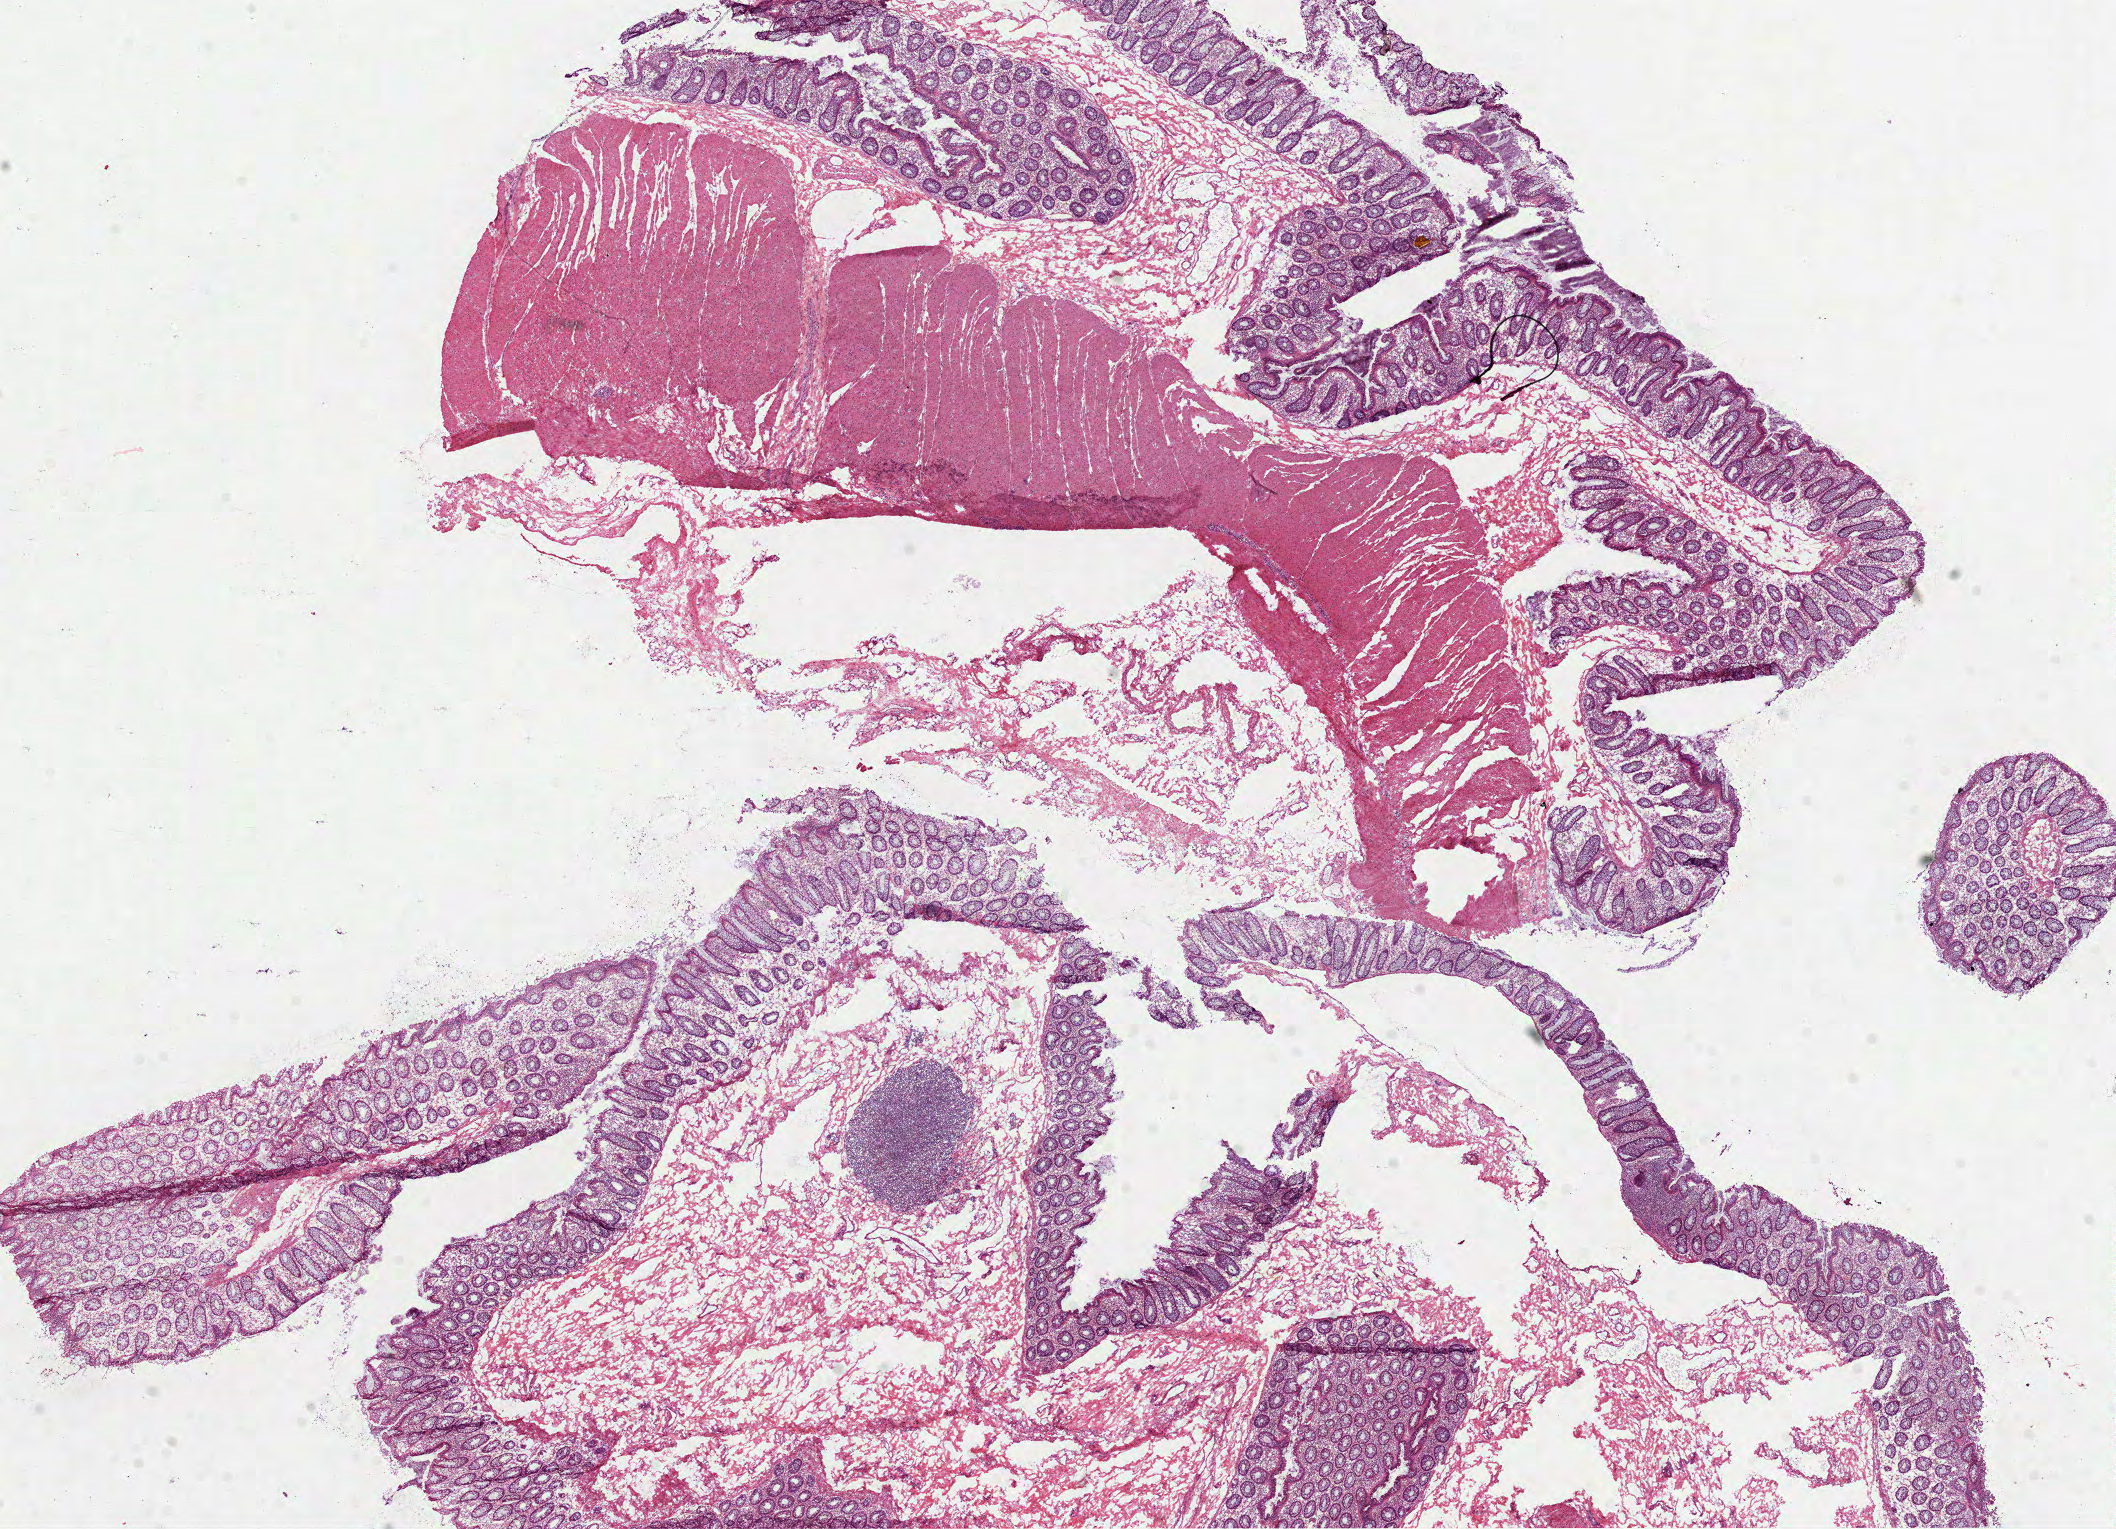
Digitized Hematoxylin and eosin (H&E) stained tissue section (whole slide) — shown as a low-resolution overview of the whole scanned area (about 17.1 x 12.3 mm, from a 40x scan), frozen section from the top of the tissue portion, sample: solid tissue normal (non-tumour tissue), colon. Male, age 68 years at initial diagnosis.
- this section: solid tissue normal sample (biorepository sample class)
- patient diagnosis: Adenocarcinoma, NOS